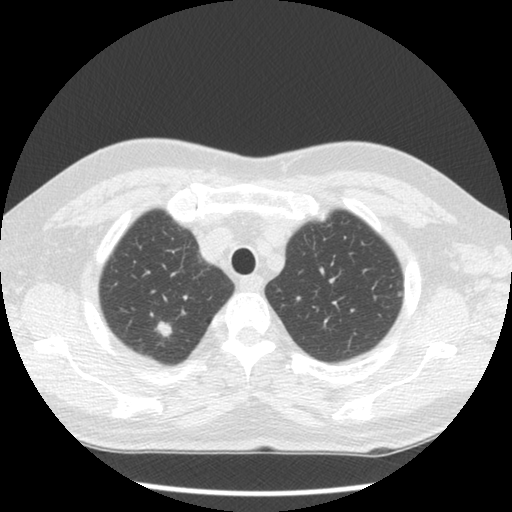
Low-dose screening chest CT, one axial slice; slice 101 of 120 in the series (ordered by position); reconstruction kernel STANDARD; 120 kVp; lung window (W 1500 / L -600 HU); 2.5 mm slice thickness; 512 × 512 image matrix, field of view 332 × 332 mm.
Structures marked on this image (expert manual segmentation):
- lesion 1 (tumor, upper lobe of right lung): box from (x=155, y=321) to (x=172, y=338) px